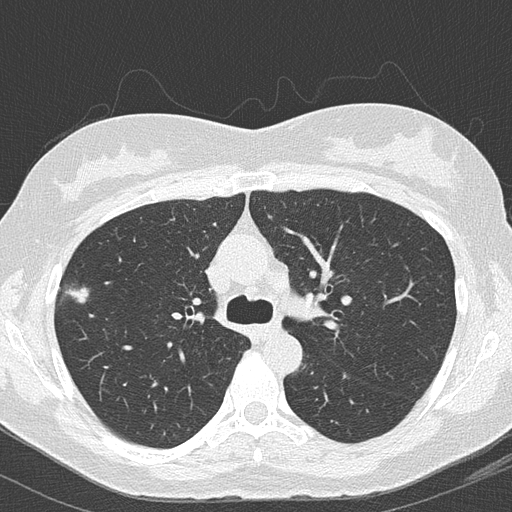
Axial slice from a low-dose chest CT screening exam; second screening round (one year after baseline); lung window (W 1500 / L -600 HU); 2 mm slice thickness; lung (sharp) reconstruction kernel (B50f). Female participant, aged 64 years at enrolment.
Lesion marked by an expert reader, bounding box [x1, y1, x2, y2] px = [48, 269, 103, 319]. Reader record for this screening exam (exam-level; its link to the box is not recorded): non-calcified nodule or mass ≥4 mm, right upper lobe, 16 × 13 mm, mixed attenuation, pre-existing on the prior screen: yes; interval growth: yes. Later outcome: lung cancer diagnosed 112 days after this screen — bronchiolo-alveolar adenocarcinoma, NOS, right upper lobe, well differentiated (G1), stage IA (AJCC 6th edition), 10 mm at pathology.